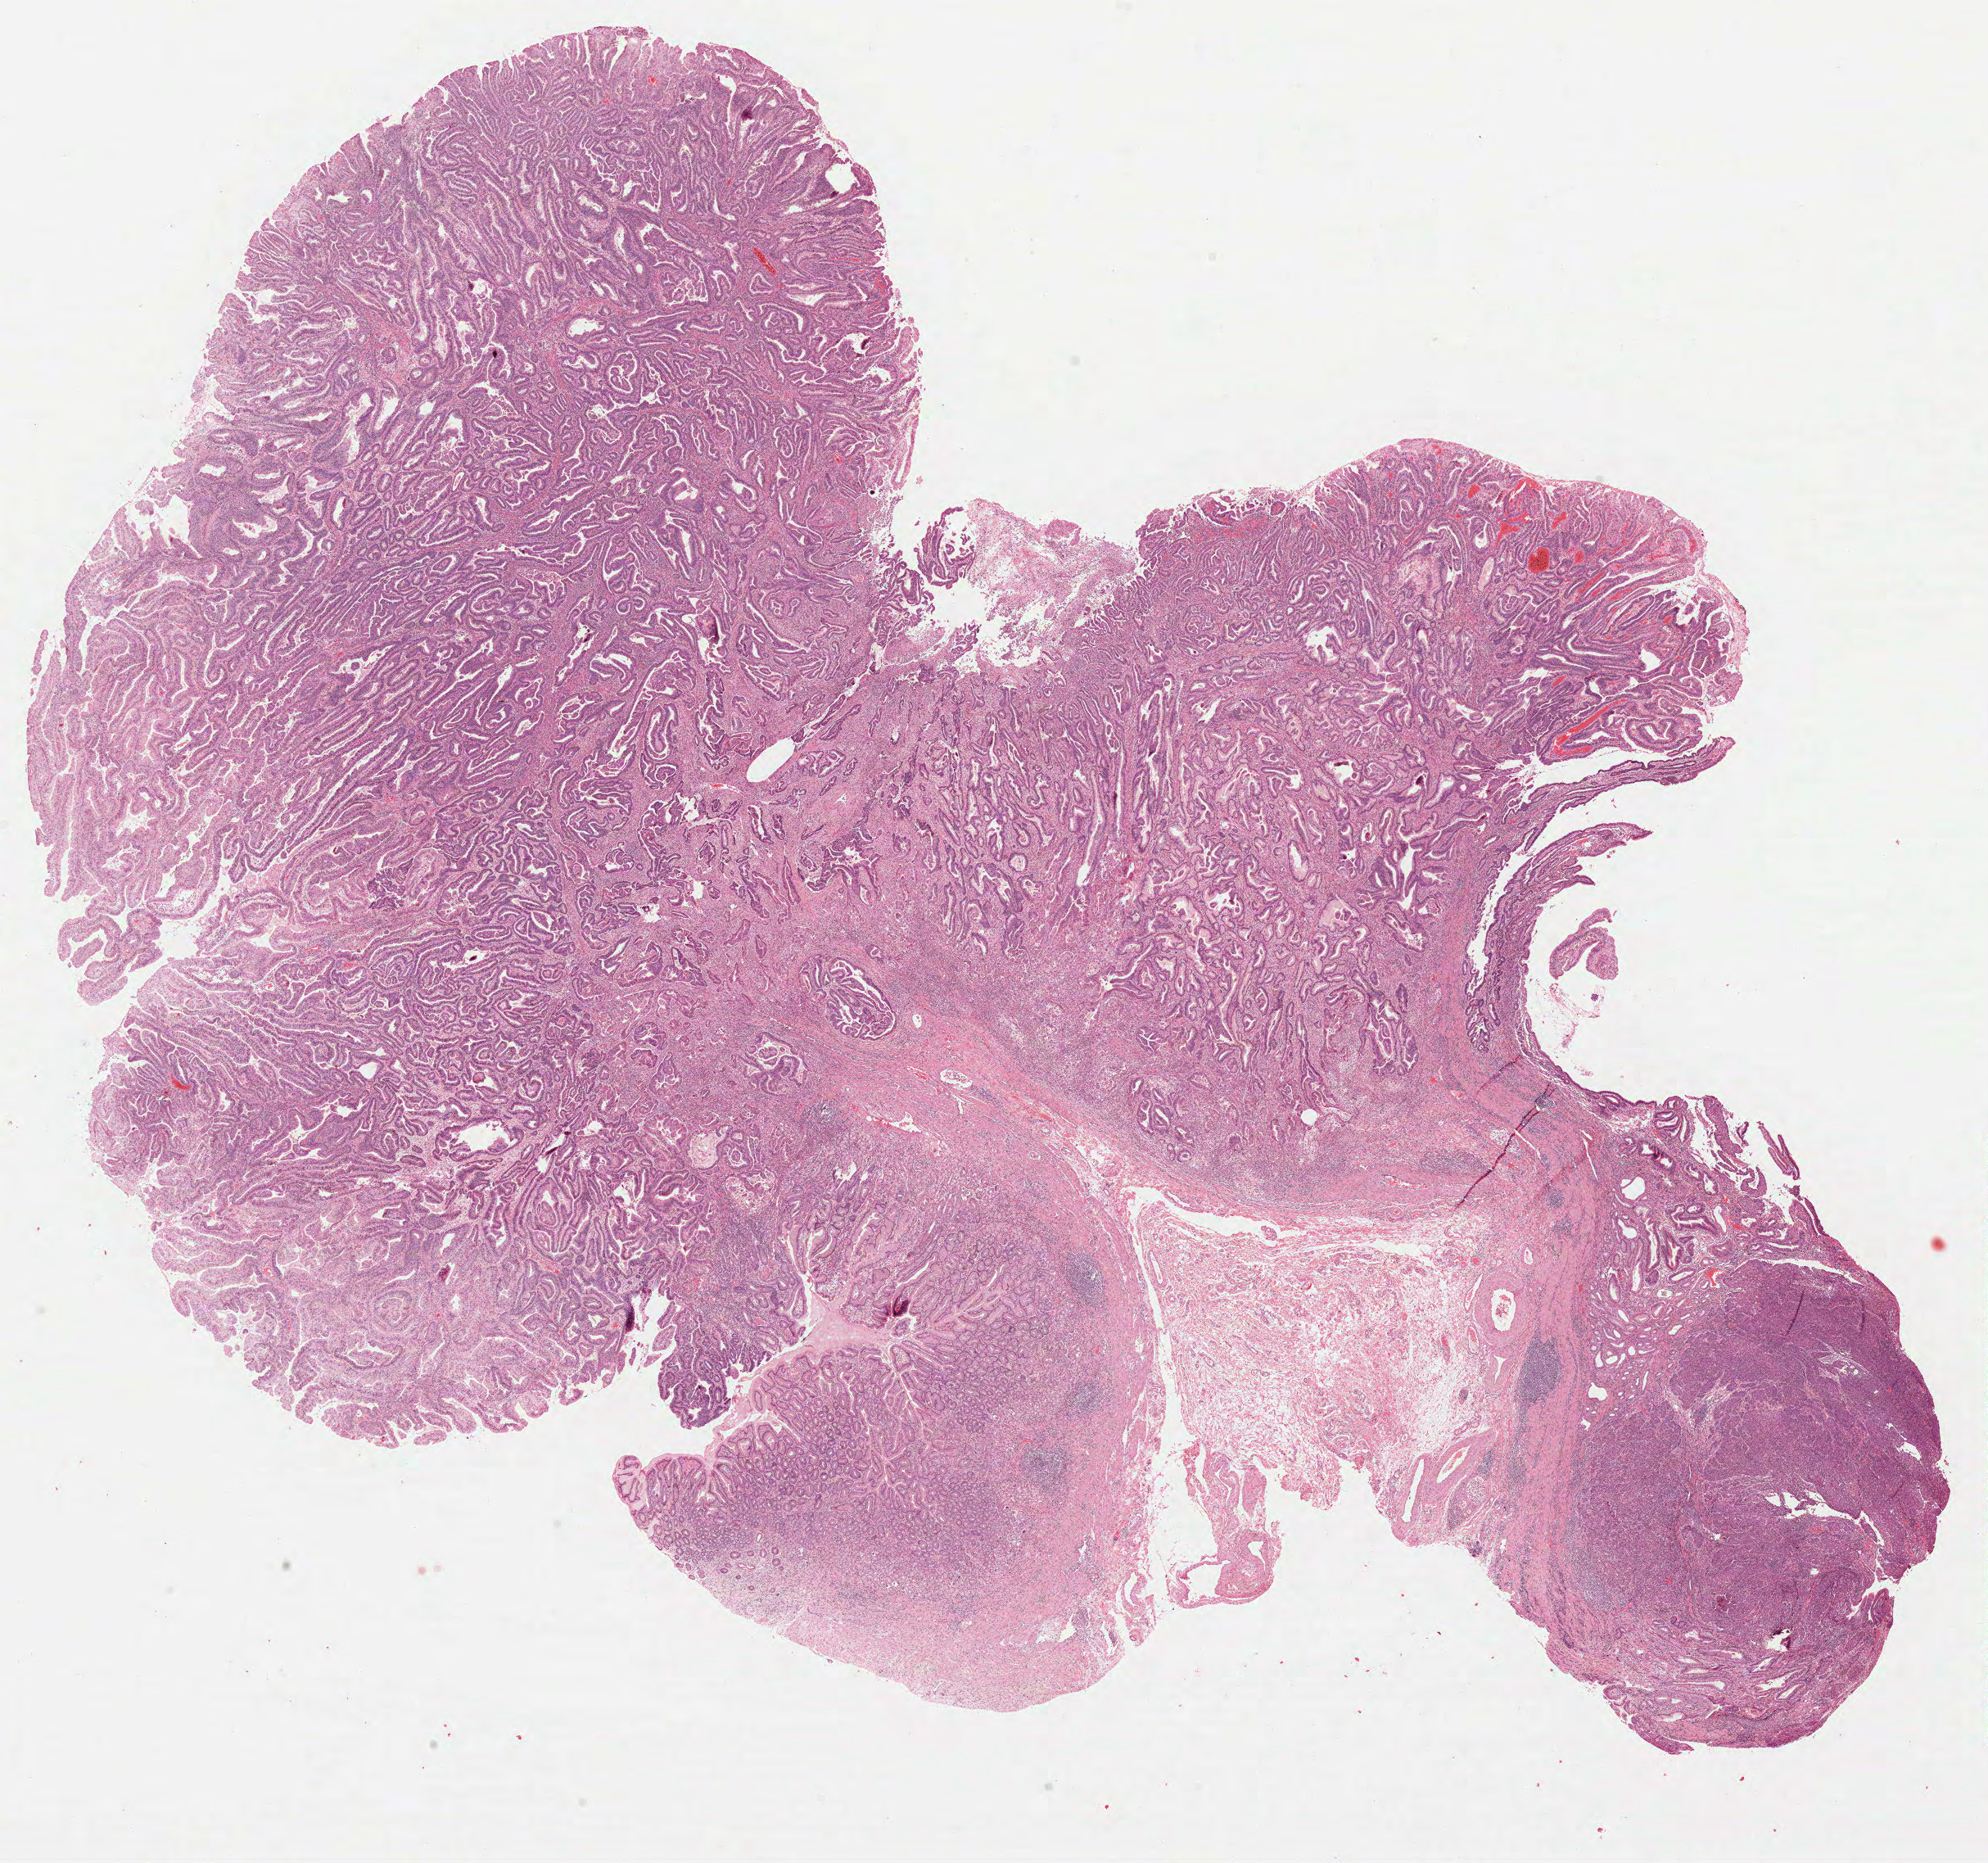
Whole-slide histology image, H&E — low-resolution overview of the scanned area, about 19.6 x 18.3 mm (slide scanned at 40x); FFPE section; primary tumour sample from the stomach. Female, age 78 years at initial diagnosis. Histologic grade: G3 (poorly differentiated).
TNM: T3 N0 M0. Histologic diagnosis: Adenocarcinoma, NOS (body of stomach). Lymph nodes positive (case pathology): 0 of 5 examined. AJCC pathologic stage: IIA (7th edition).